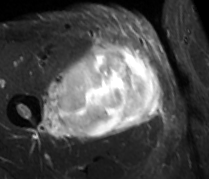
MRI of an extremity soft-tissue mass, one axial slice; position 41 of 89 along the scan axis; STIR; MR volume resampled by the dataset authors to the PET/CT grid (not the native acquisition matrix); 209 × 179 image matrix. Male patient. Case-level facts recorded for this patient, not image findings: histological type: undifferentiated - pleiomorphic; grade: high; site of the primary tumour: right thigh.
Outlined on this slice (expert contour drawn on MRI and transferred to this co-registered scan by the dataset authors):
- gross tumour volume including surrounding oedema: box from (x=39, y=41) to (x=163, y=140) px
- gross tumour volume (mass): (x=57, y=43)–(x=161, y=138)